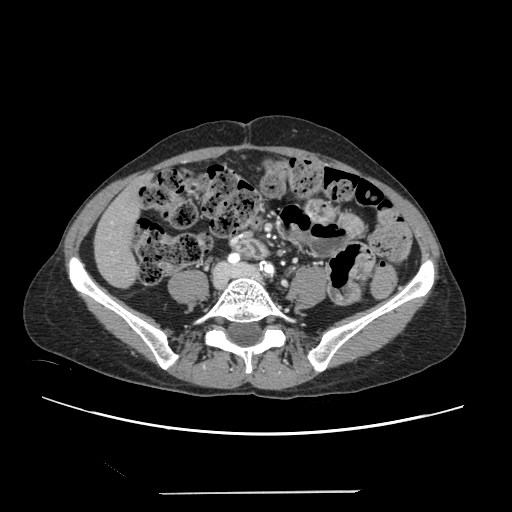
Contrast-enhanced abdominal CT, one axial slice. Position 29 of 240 along the scan axis. Intravenous contrast given. Soft-tissue window (W 400 / L 40 HU). 1.25 mm slice thickness. 512 × 512 image matrix, field of view 371 × 371 mm. Female patient, age 60 years. Case-level facts recorded for this patient, not image findings: diagnosis: colorectal cancer liver metastases, imaged before liver resection; multiple liver metastases: no.
Annotated regions visible in this slice (expert manual segmentation):
- liver: box from (x=96, y=181) to (x=142, y=286) px
- planned liver remnant (the part of the liver to remain after resection): (x=95, y=180)–(x=143, y=287)
- portal vein (with intrahepatic branches): (x=111, y=221)–(x=116, y=253)